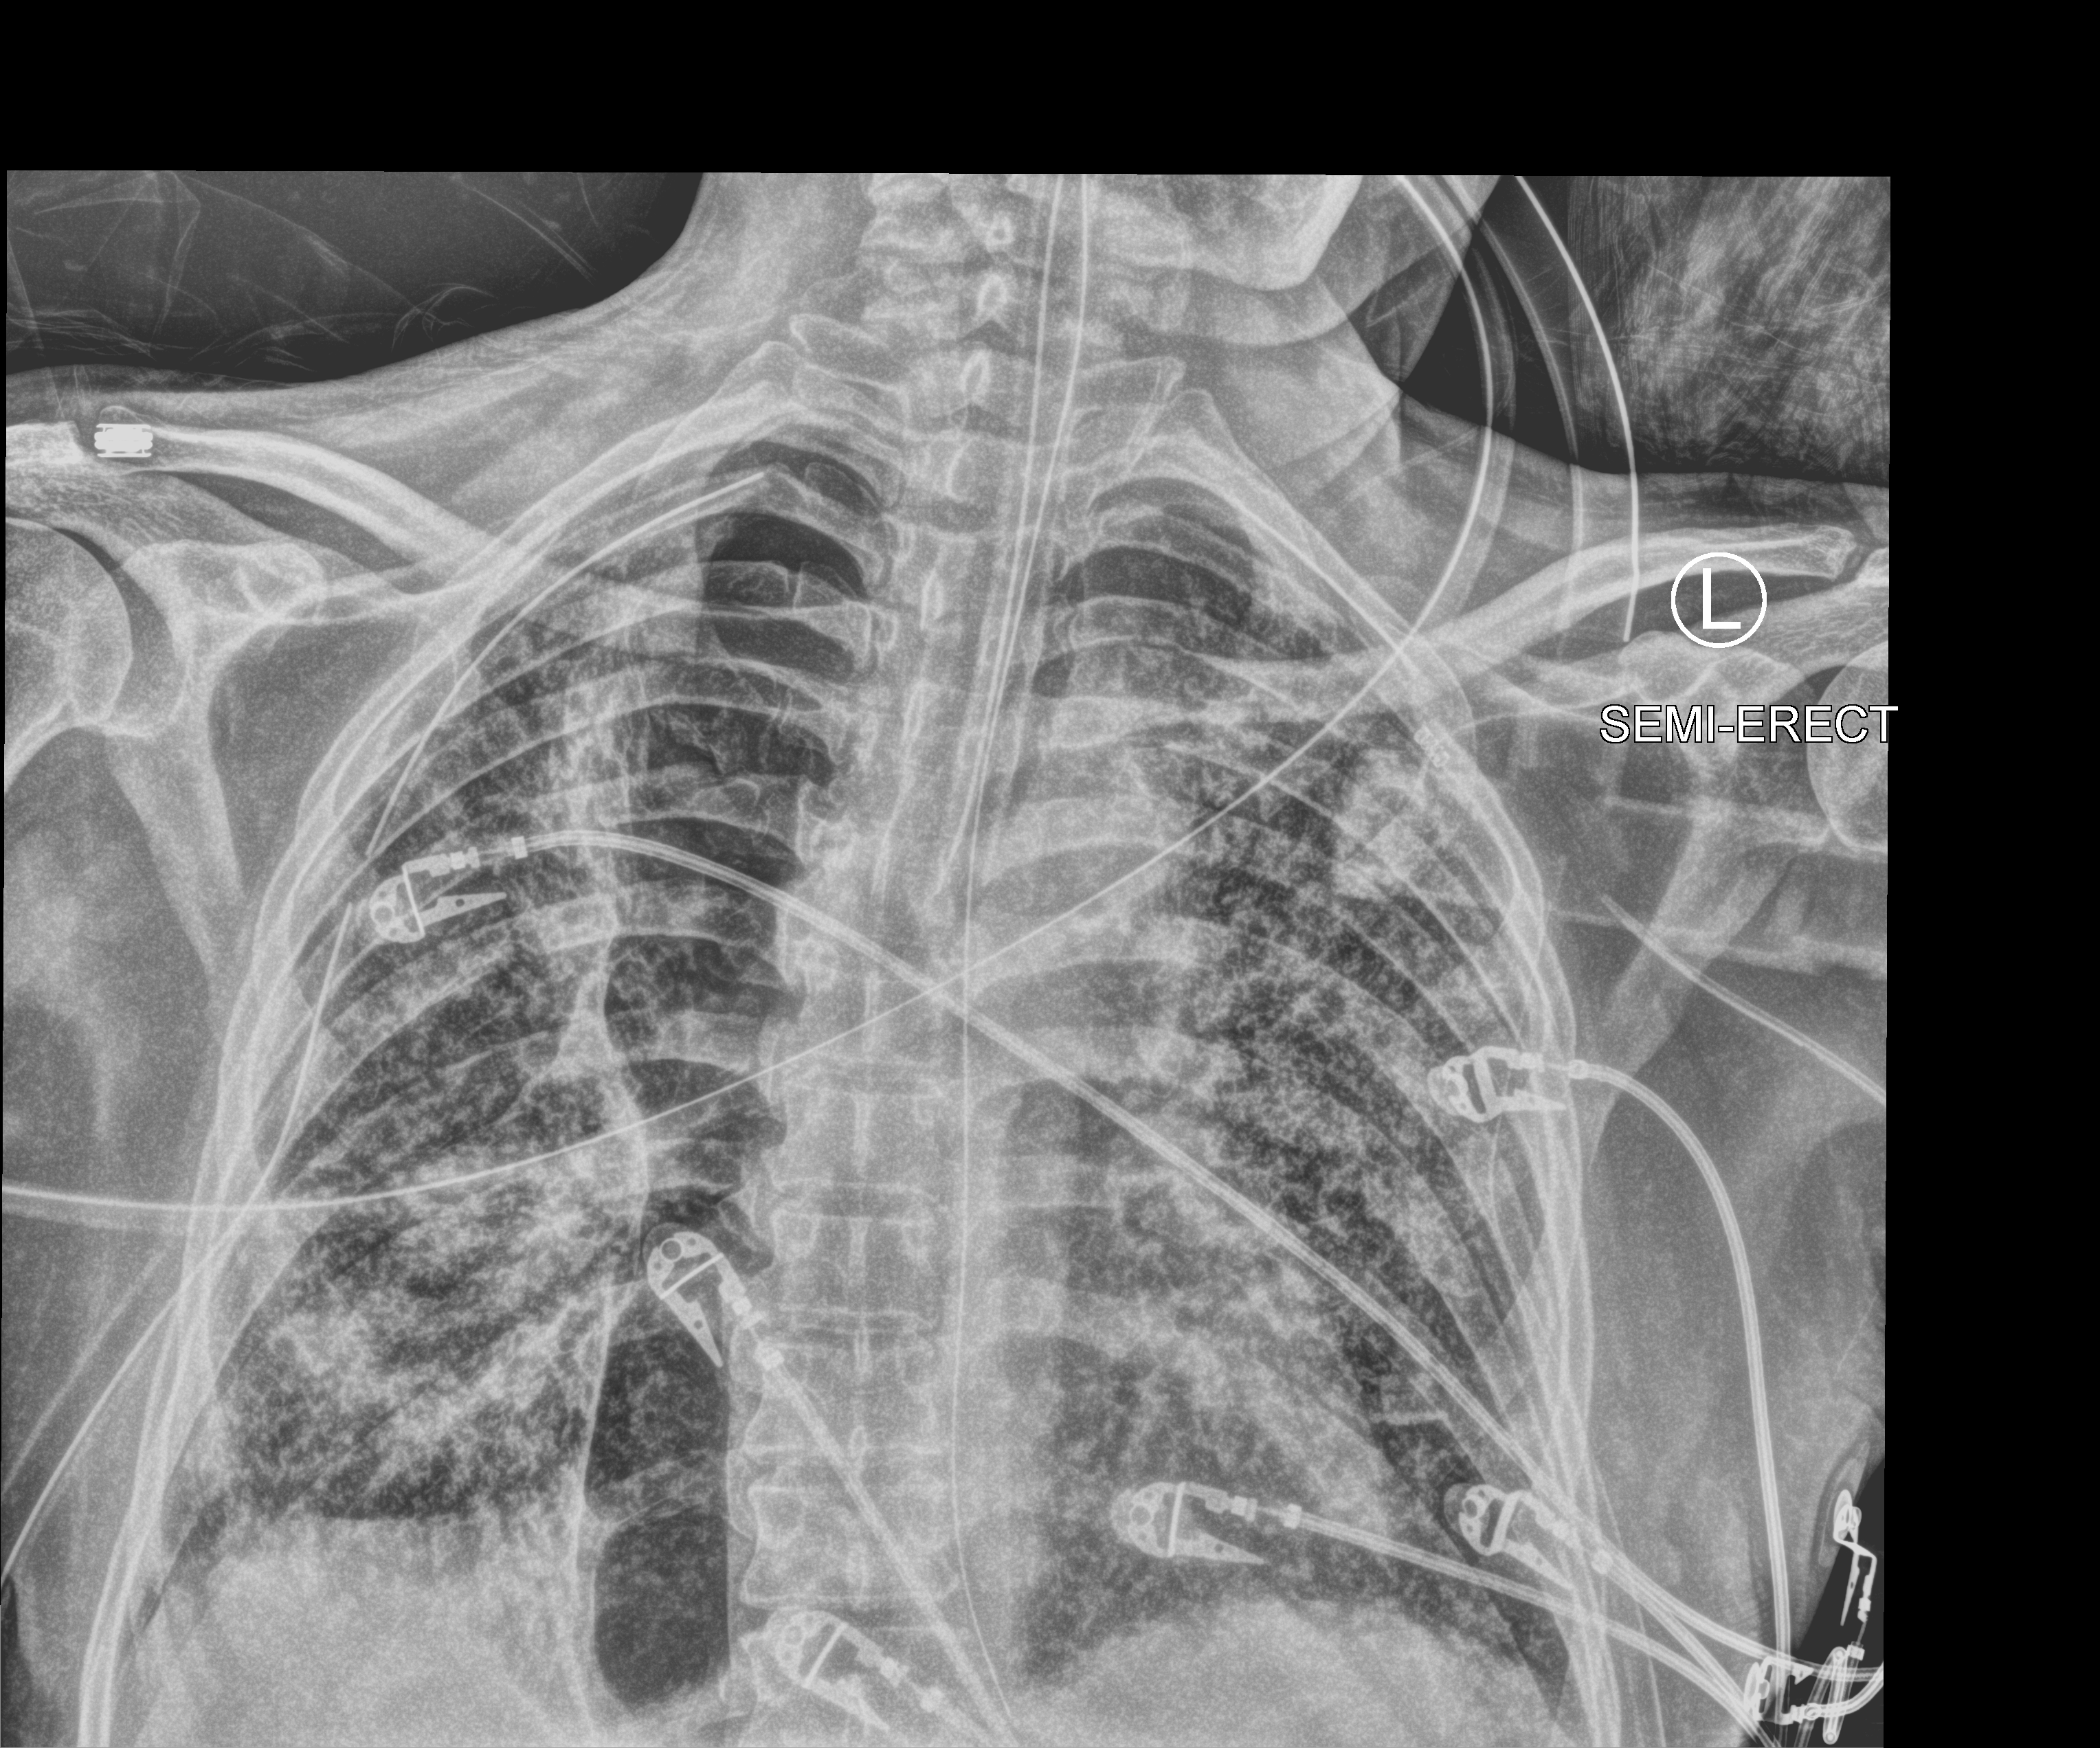
Bedside chest radiograph (computed radiography); anteroposterior (AP) projection. Male patient hospitalised with COVID-19, age 60–74 years.
From the hospital-stay record, not from the radiograph (when in the stay this image was taken is not recorded): mechanically ventilated during this hospital stay: yes.